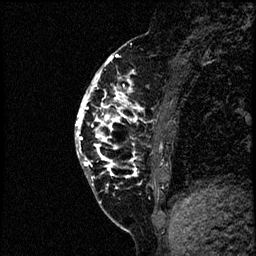
Breast MRI (dynamic contrast-enhanced), one sagittal slice. Dynamic contrast-enhanced study with each time point stored as its own series, time point 2 of 4 at this slice position (early post-contrast, ordered by acquisition time). 1.5 T. TE 4.2 ms, TR 17.6 ms. 2 mm slice thickness. 256 × 256 image matrix, field of view 200 × 200 mm. Patient: female, 40 years. Case-level facts recorded for this patient, not image findings: setting: breast cancer imaged before/during neoadjuvant chemotherapy; receptor status: HER2-positive.
Structures marked on this image (semi-automatic segmentation, software-assisted and operator-edited):
- analysis volume of interest (the breast-tissue region the enhancement analysis was run in; not a lesion): bounding box (x1, y1, x2, y2) in pixels: (76, 56, 197, 205)
- tumour enhancement mask (voxels above the 100 % enhancement threshold inside the analysis volume of interest): (76, 56, 143, 180)